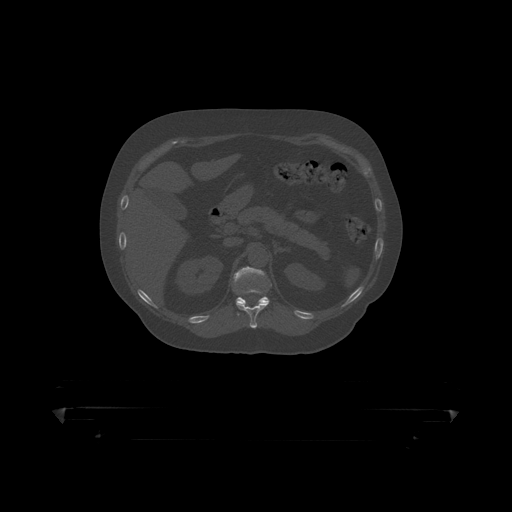
CT including the spine, one axial slice. Slice 184 of 390 in the series (ordered by position). Reconstruction kernel STANDARD. Bone window (W 1800 / L 400 HU). 512 × 512 image matrix, field of view 650 × 650 mm. Male patient, age 60 years. Case-level facts recorded for this patient, not image findings: primary cancer: prostate.
Annotated regions visible in this slice (semi-automatically segmented with operator editing):
- T11 vertebra: bounding box [x1, y1, x2, y2] px = [236, 278, 272, 319]
- T12 vertebra: [234, 267, 270, 316]